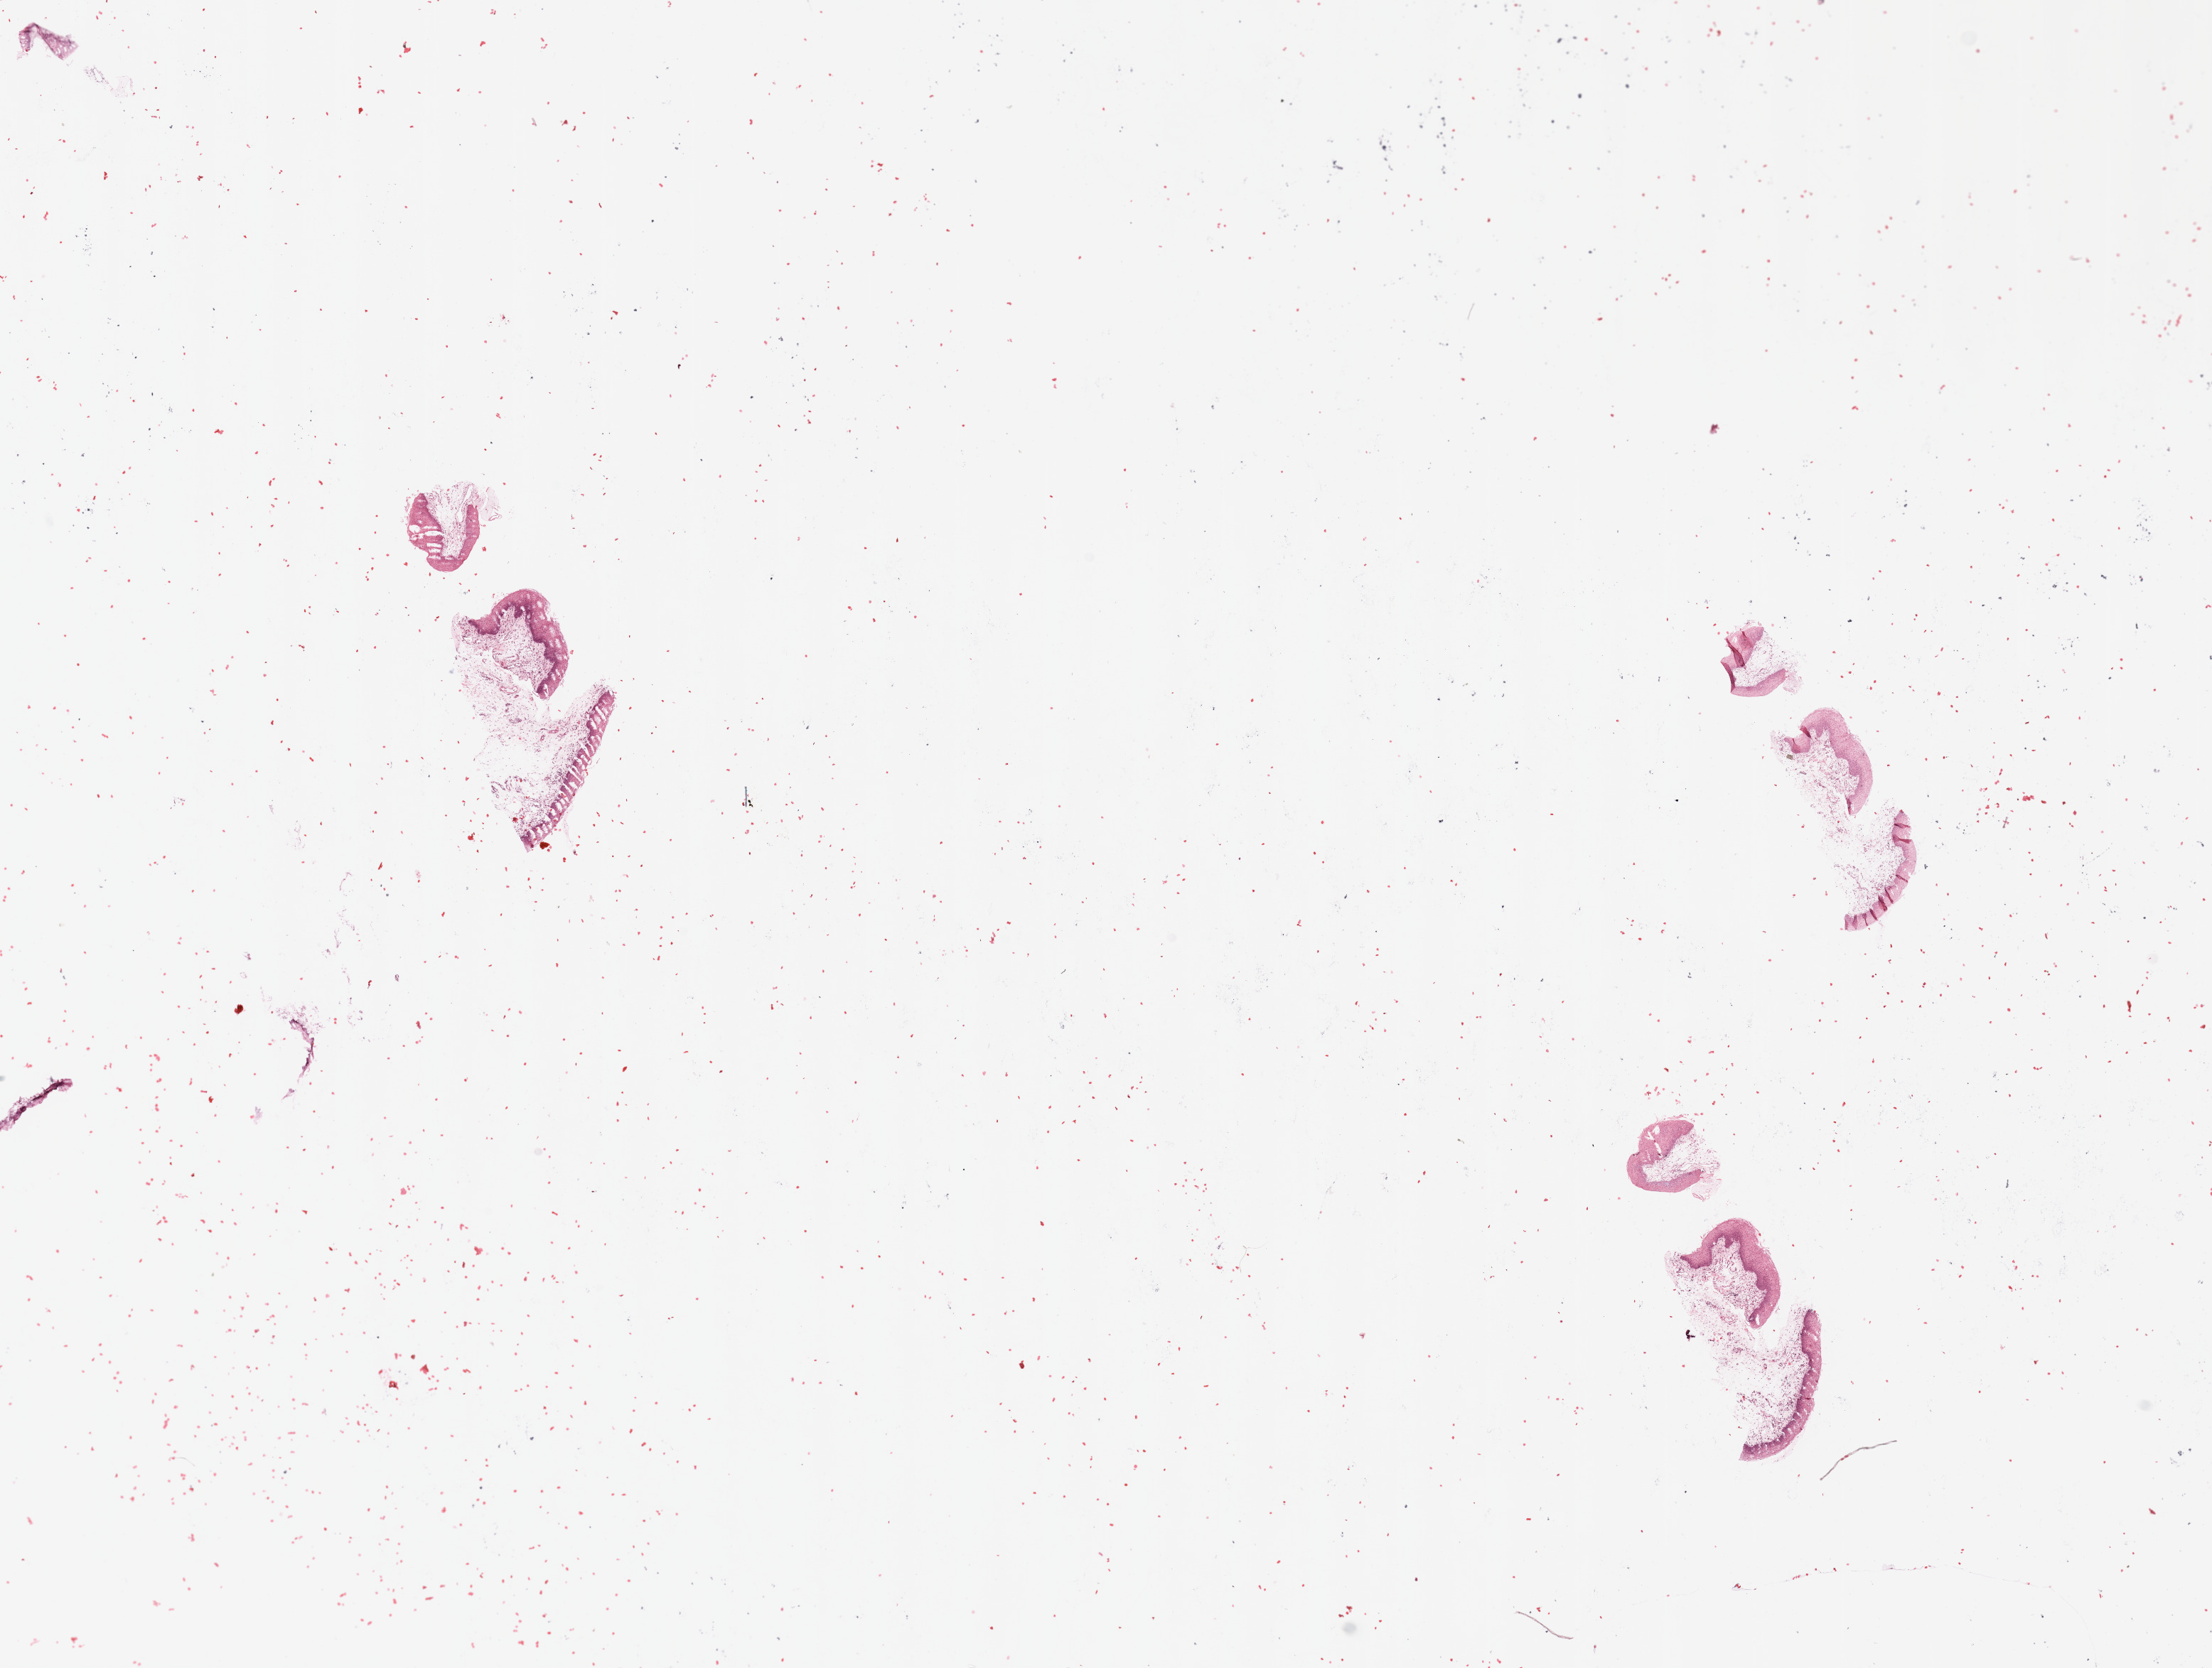
Hematoxylin and eosin (H&E) stained whole-slide image, shown as a low-resolution overview of the whole scanned area (about 24.6 x 18.6 mm, acquisition: 20x scan); normal (non-tumour) tissue sample, head and neck. Male, 67 y/o.
This section: normal (non-tumour) tissue from the same patient. Patient diagnosis: Squamous cell carcinoma, NOS (larynx, NOS).